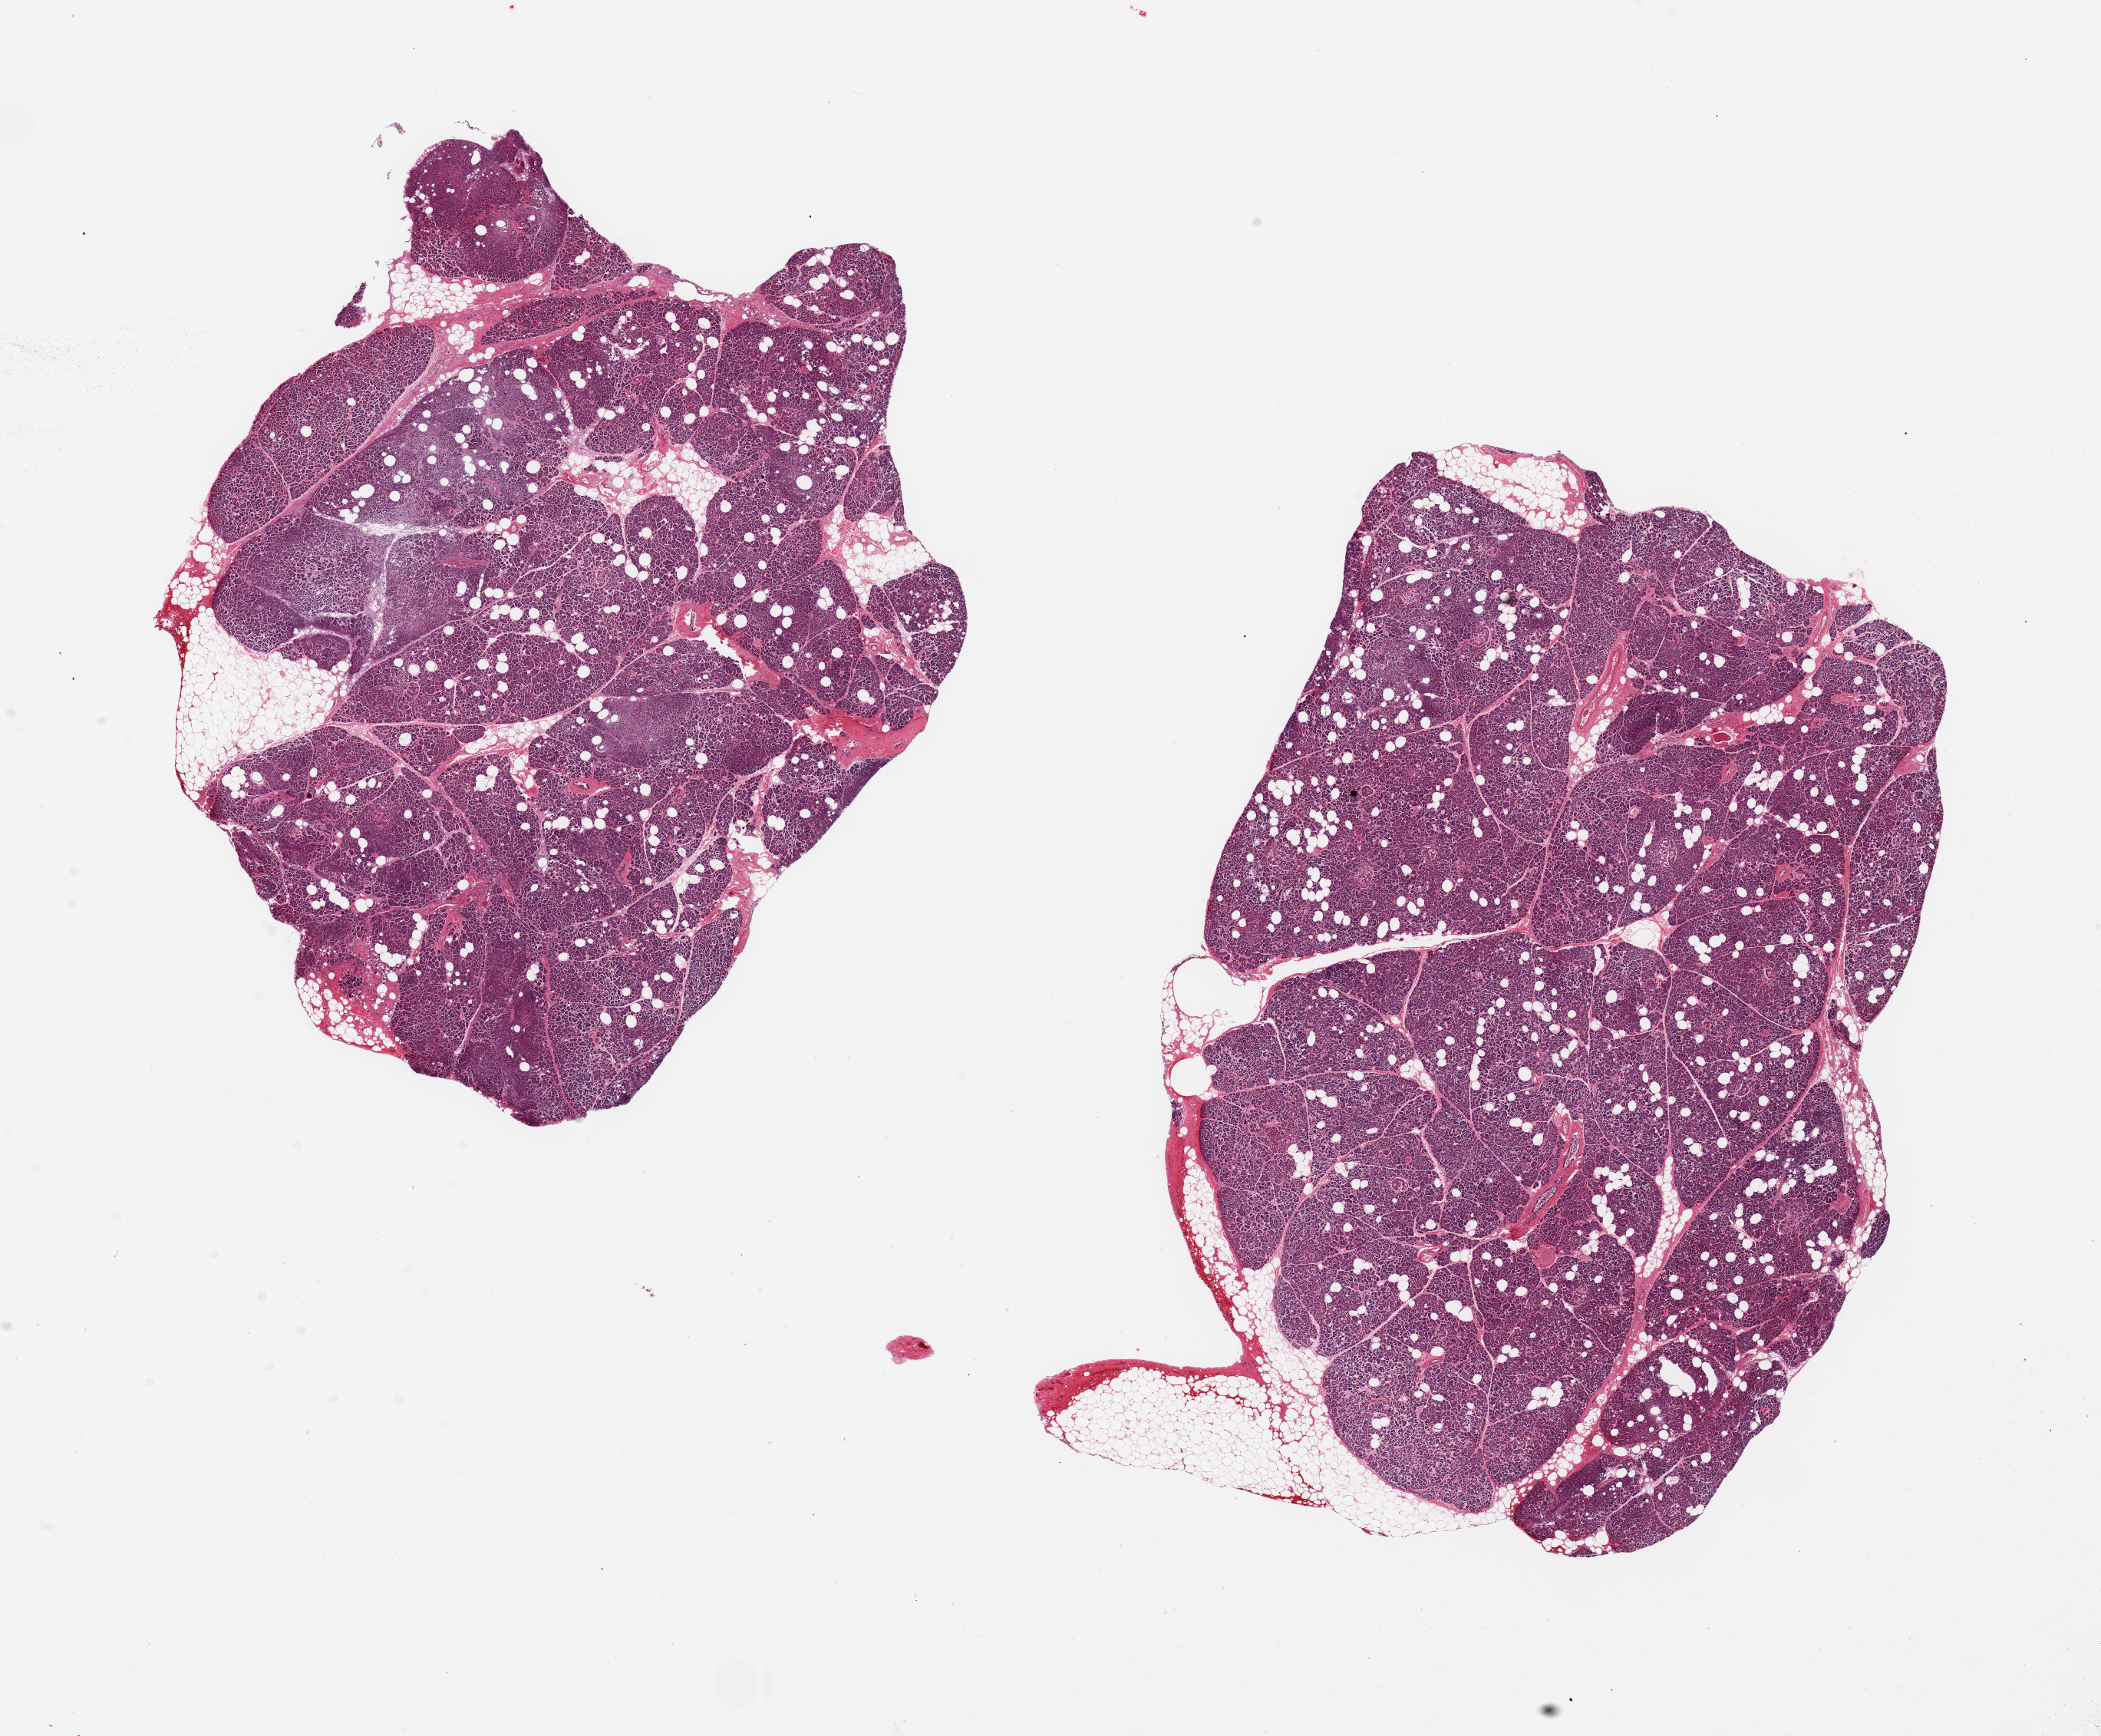
Whole-slide image, H&E stain — a low-resolution overview of the entire scanned area, about 21.7 x 17.9 mm (from a 20x scan). PAXgene-fixed, paraffin-embedded tissue. Target tissue: pancreas. Tissue donor sample. Donor sex: female.
Pathologist's review note for this sample: 2 ~10x7mm aliquots, relatively clean, mild peripancreatic saponification.